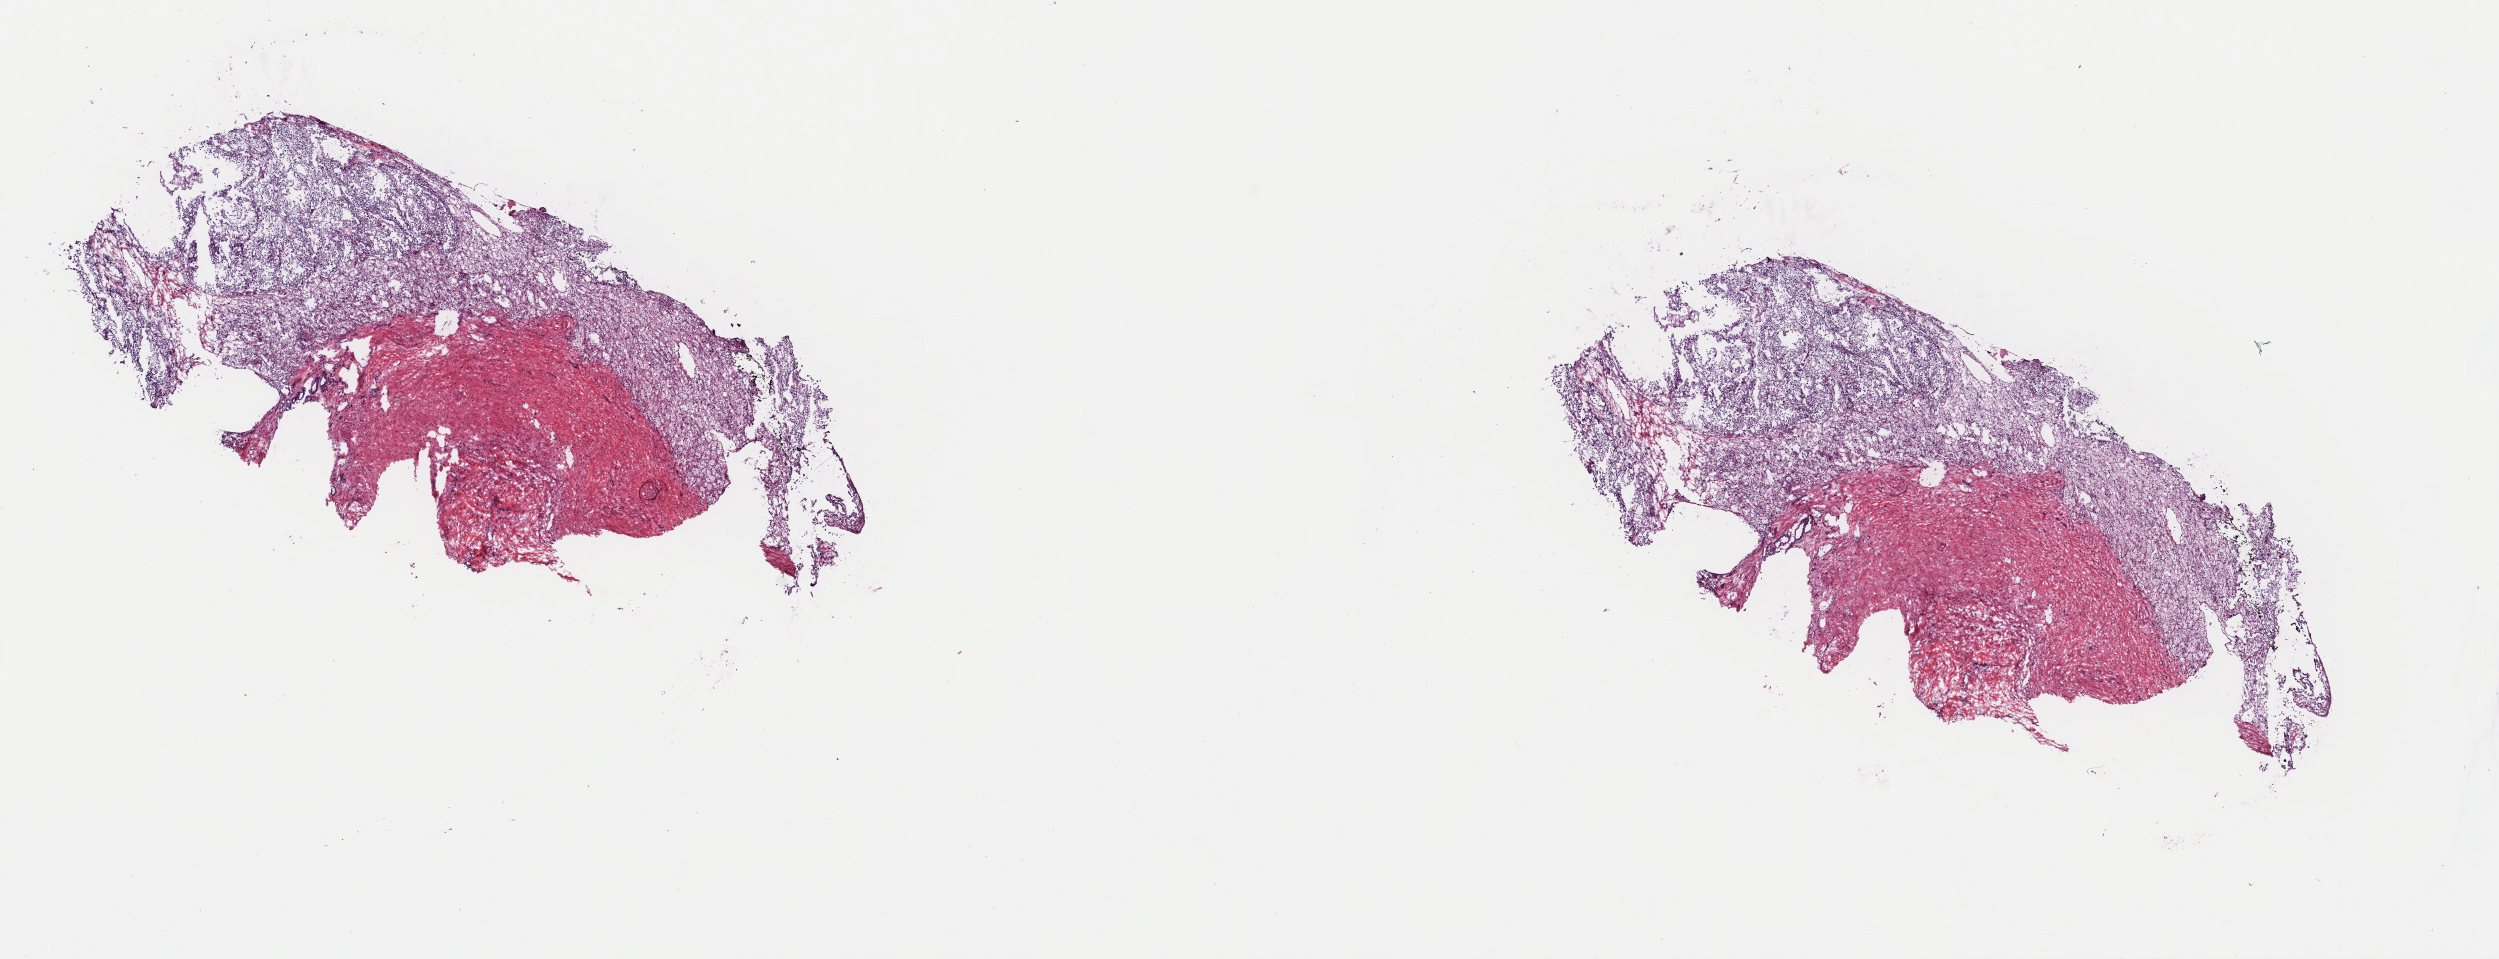
Whole-slide histology image, H&E-stained, a low-resolution overview of the entire scanned area, about 19.7 x 7.6 mm; frozen section from the top of the tissue portion; sample: primary tumour, kidney. Male, age 47 years at initial diagnosis. Histologic grade: G3 (poorly differentiated). Composition of this section per pathologist review: tumour cells 59%, tumour nuclei 90%, normal cells 1%, stromal cells 40%, necrosis 0%. Infiltration values recorded for this section: lymphocyte infiltration 2%, monocyte infiltration 0%, neutrophil infiltration 0%.
AJCC pathologic stage: I (7th edition). Pathologic diagnosis: Renal cell carcinoma, NOS. Laterality: left.